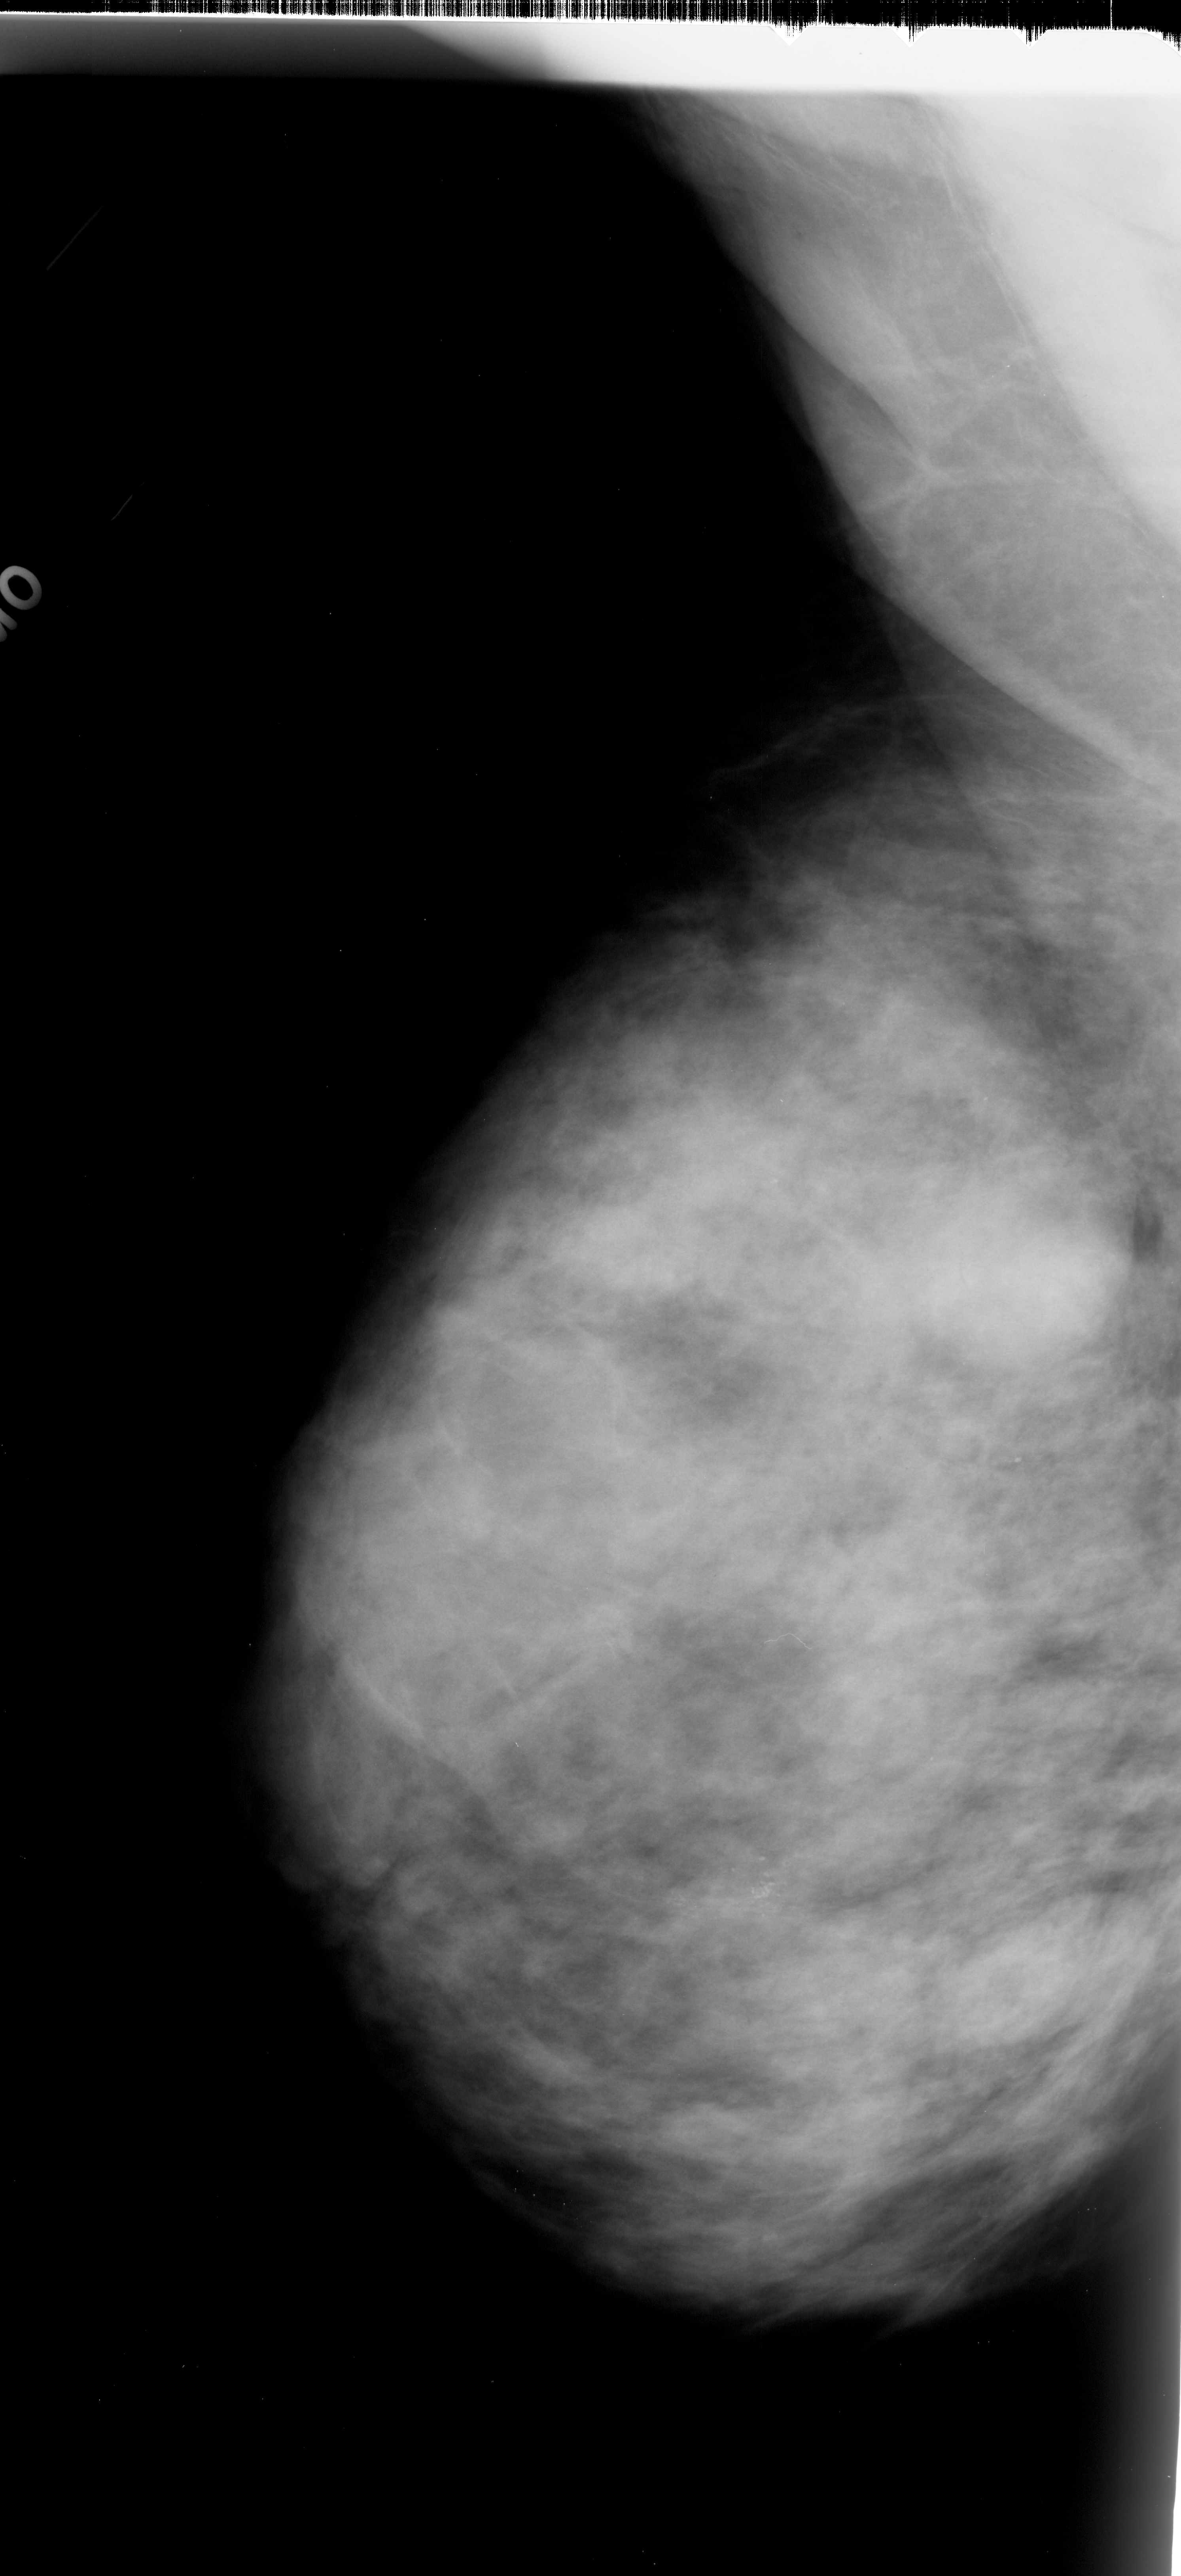
Scanned film-screen mammogram. Left breast. MLO view. BI-RADS breast density category 4 (scale 1–4). 1181 × 2576 image matrix.
Expert-marked regions of interest on this image (one box per marked abnormality):
- calcifications, morphology pleomorphic, distribution clustered; BI-RADS assessment category 4; pathology (as recorded): malignant: bounding box <641,1846,811,1946> (left, top, right, bottom; pixels)